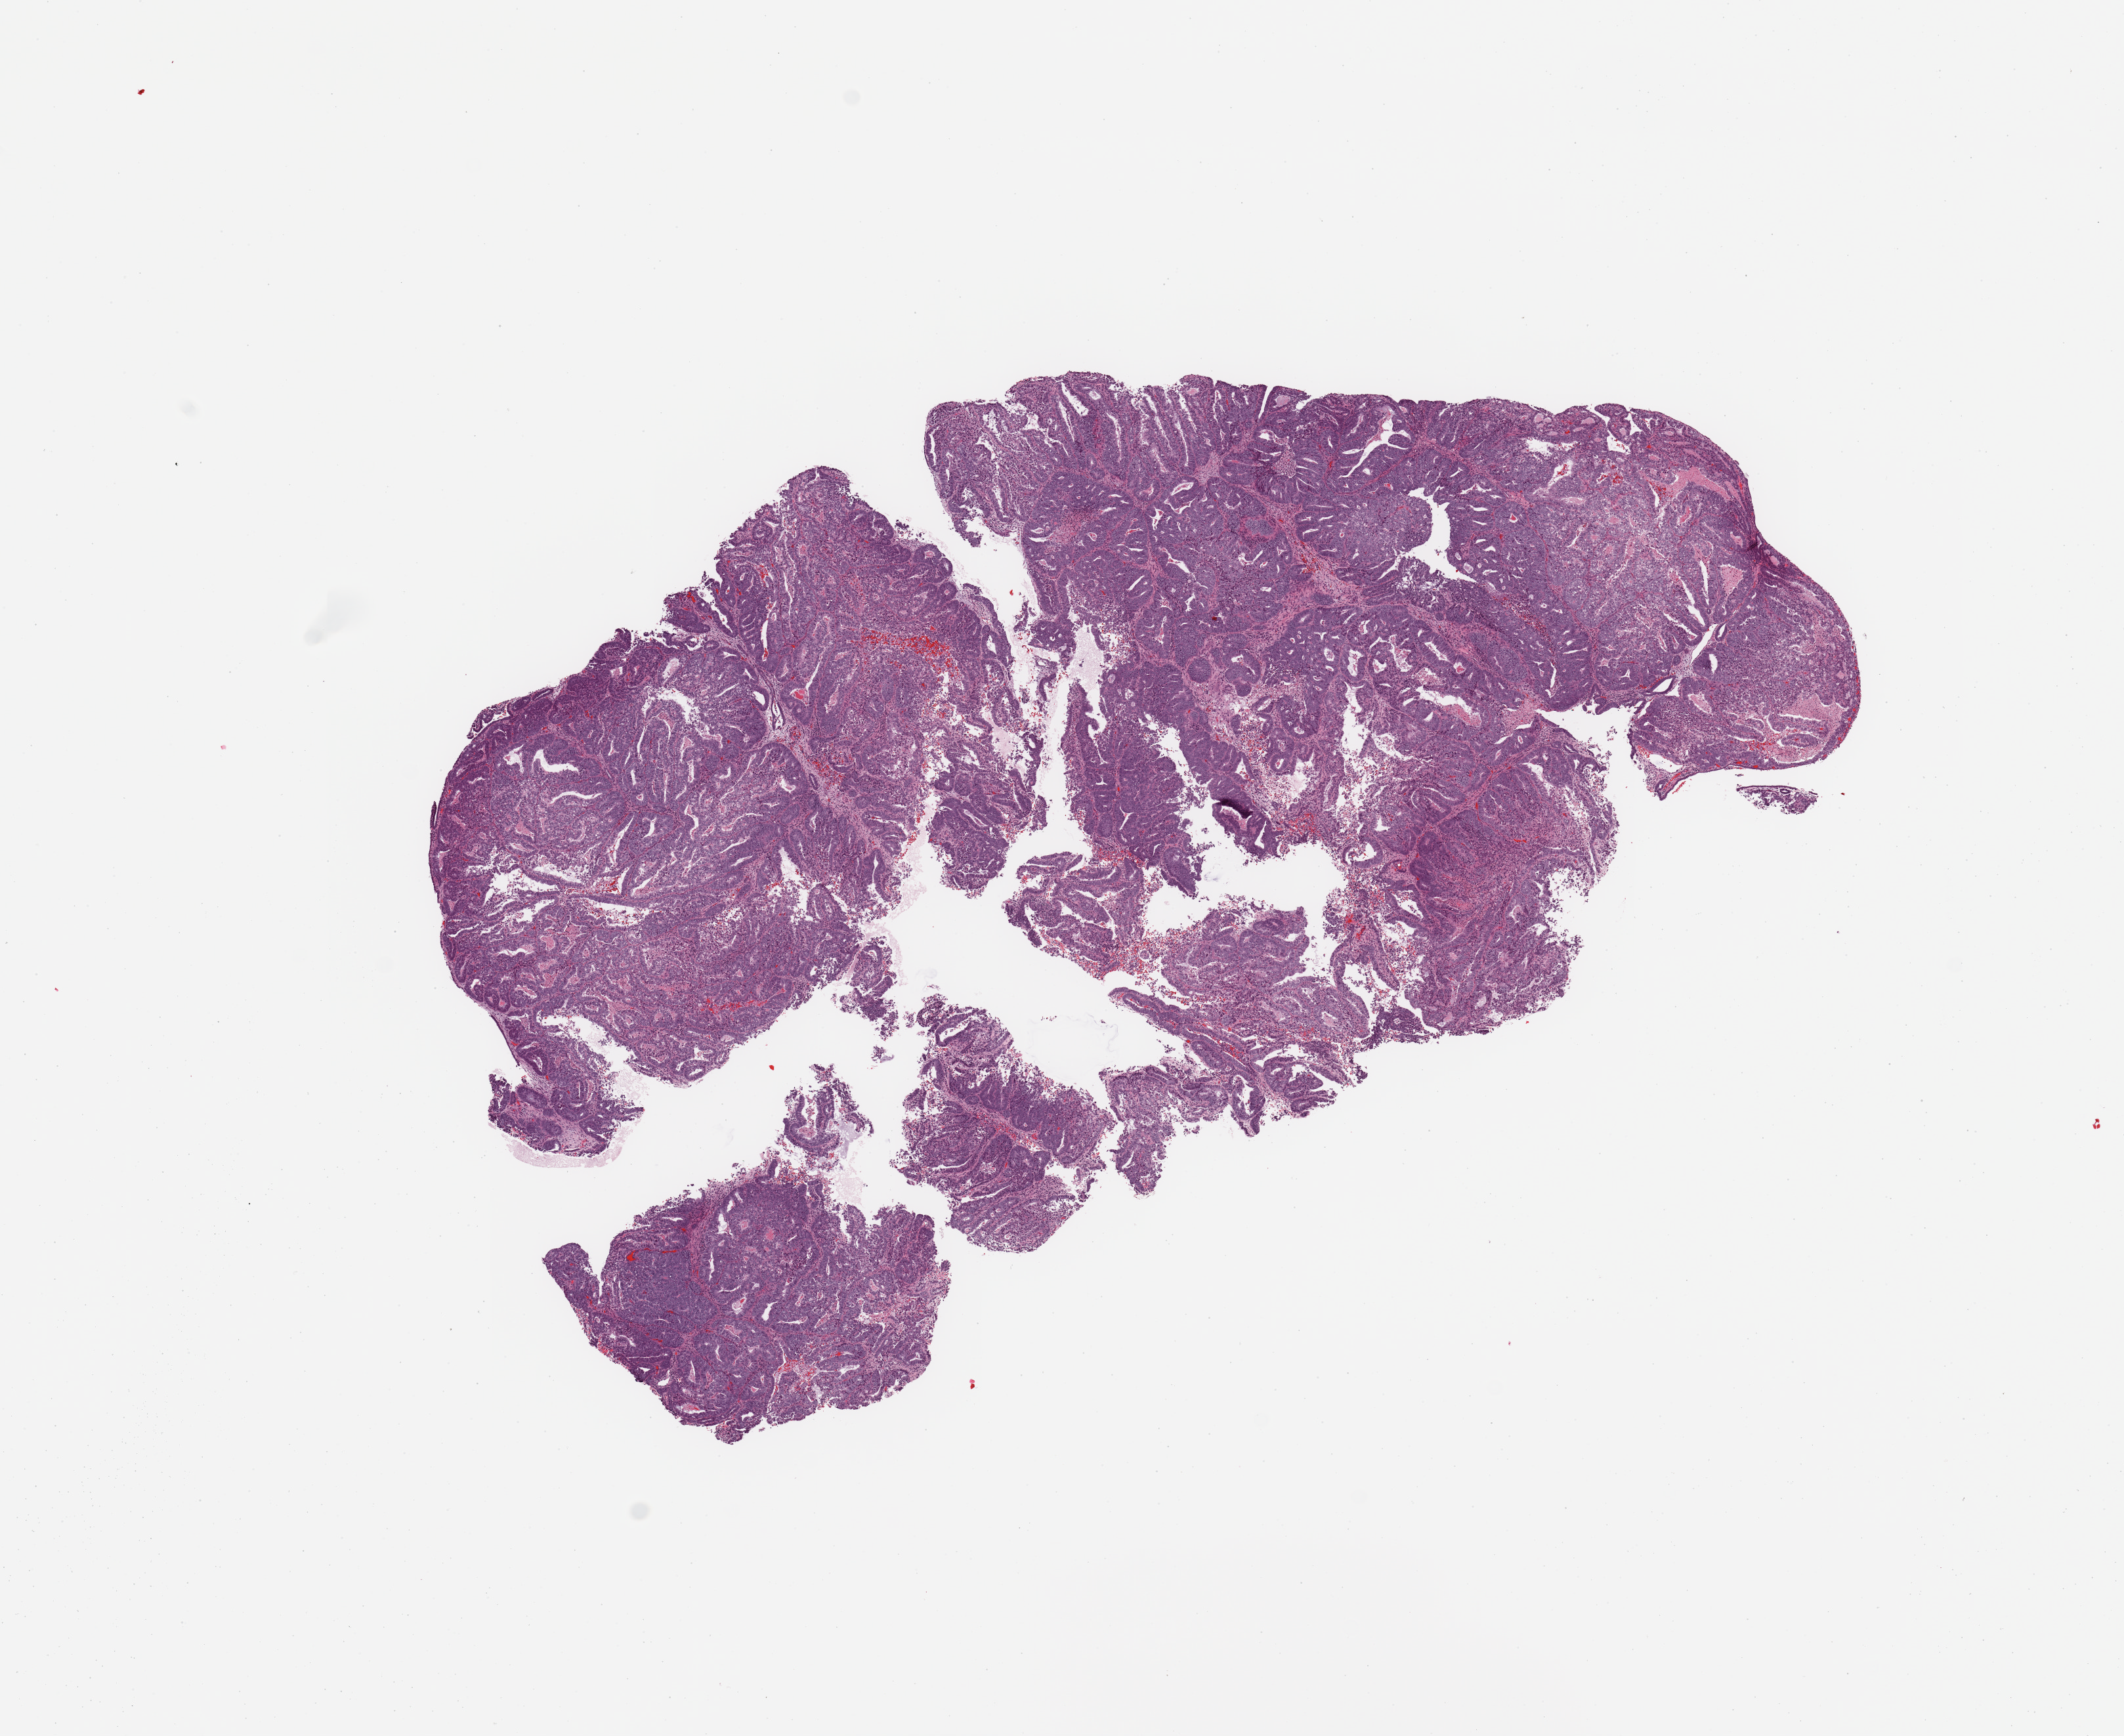
Whole-slide histology image, H&E-stained, low-resolution overview of the scanned area, about 12.8 x 10.5 mm (acquisition: 20x scan), tumour tissue sample, uterus. 57-year-old female patient. Histologic grade: G3 (poorly differentiated).
Histologic diagnosis: Endometrioid adenocarcinoma, NOS. AJCC pathologic stage: I.